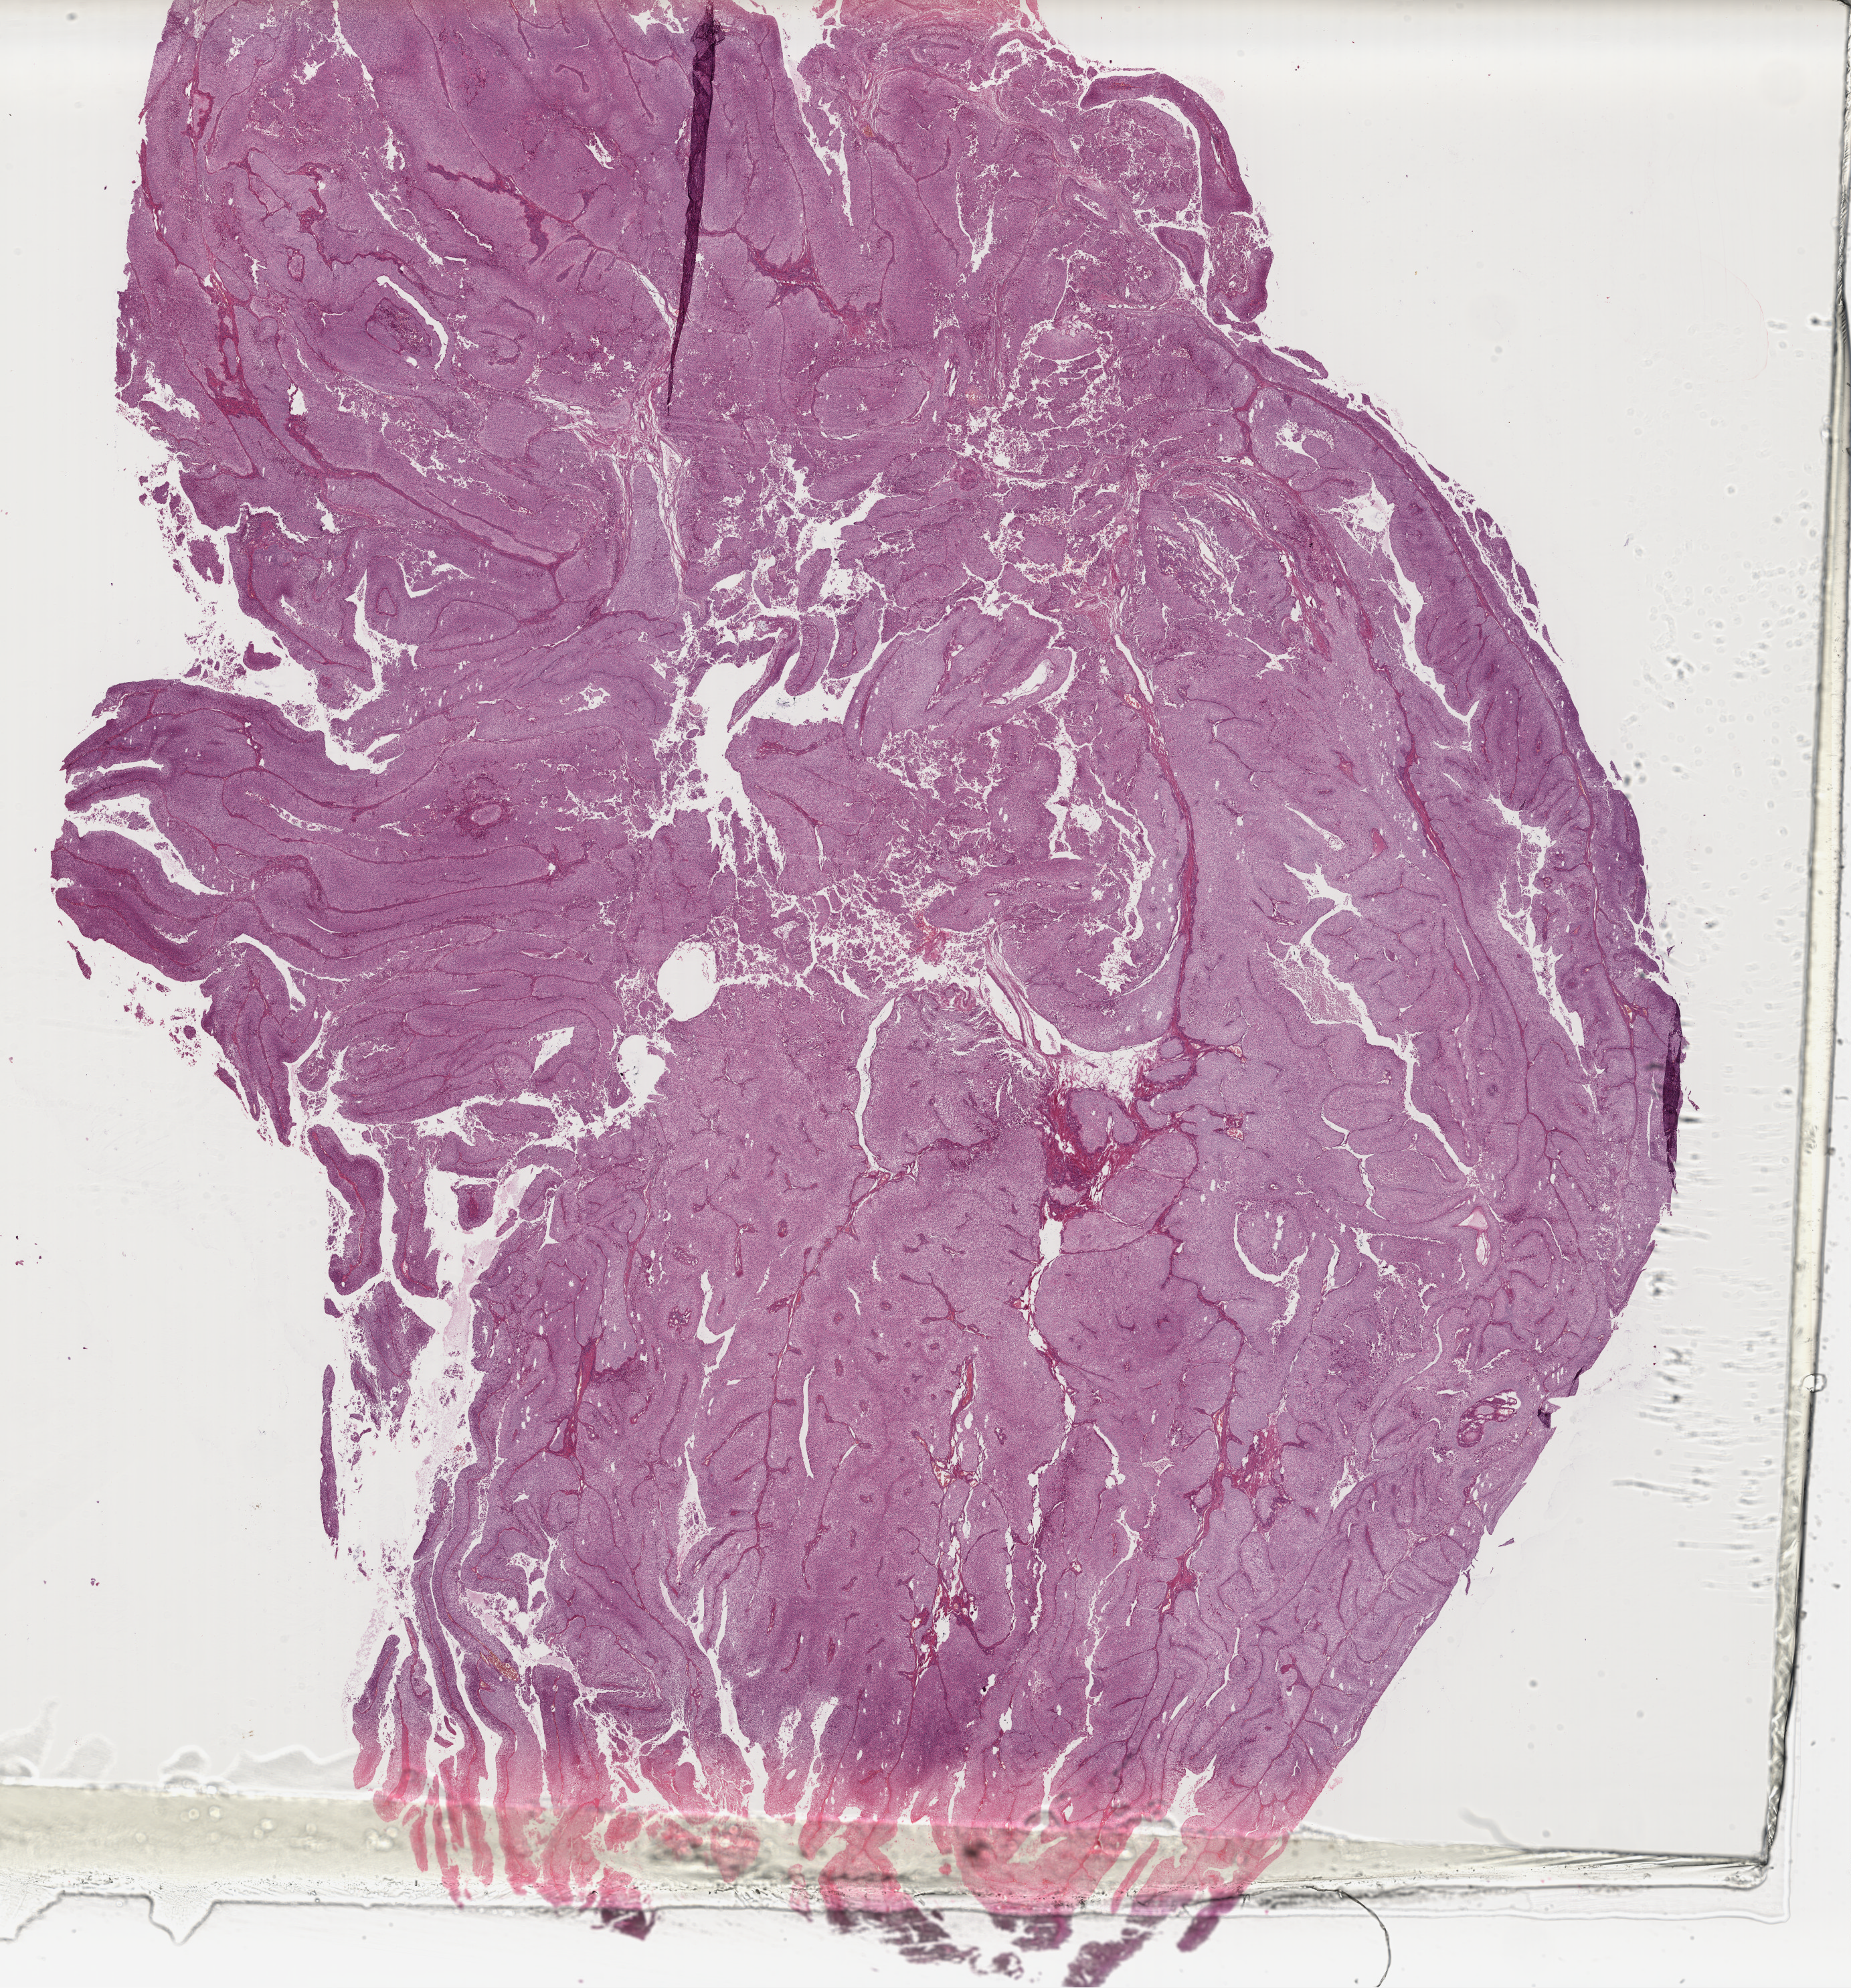
Digitized H&E tissue section (whole slide) — whole scanned area (about 21.7 x 23.3 mm) shown as a low-resolution overview; formalin-fixed paraffin-embedded (FFPE) diagnostic section; sample: primary tumour, bladder. Male, age 34 years at initial diagnosis. Histologic grade: low grade.
* AJCC pathologic stage: III (7th edition)
* diagnosis: Papillary transitional cell carcinoma